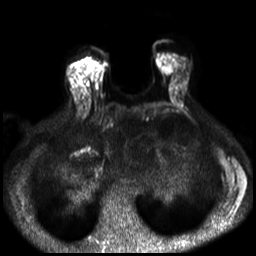
Breast MRI, one axial slice. Position 10 of 30 along the scan axis. Diffusion-weighted series; image 2 of 4 stored at this slice position (different b-values; order by instance number). 3 T. 4 mm slice thickness. 256 × 256 image matrix, field of view 320 × 320 mm. Female patient.
Annotated regions visible in this slice (expert manual segmentation):
- tumour on diffusion-weighted imaging: bounding box <95,68,101,77> (left, top, right, bottom; pixels)